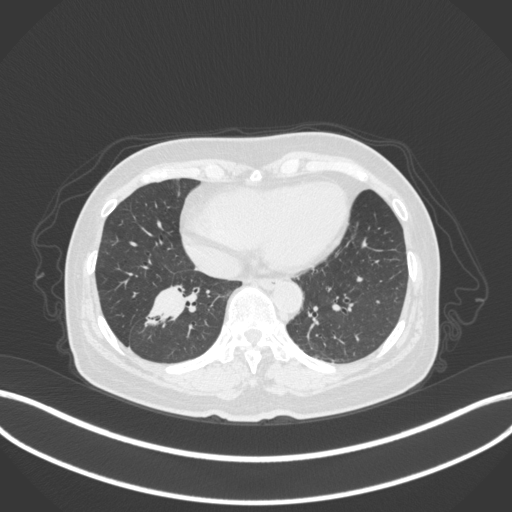
Chest CT, one axial slice. Reconstruction kernel B31f. Lung window (W 1500 / L -600 HU). 1 mm slice thickness. 512 × 512 image matrix, field of view 400 × 400 mm. Patient: female, 67 years. From the clinical record (not read from this slice): clinical TNM (as recorded): T1c N1 M0; histopathological grade: G2-3.
Structures marked on this image (rectangle marked by the reading radiologist):
- lung tumour (recorded histology: adenocarcinoma): box from (x=138, y=280) to (x=201, y=332) px